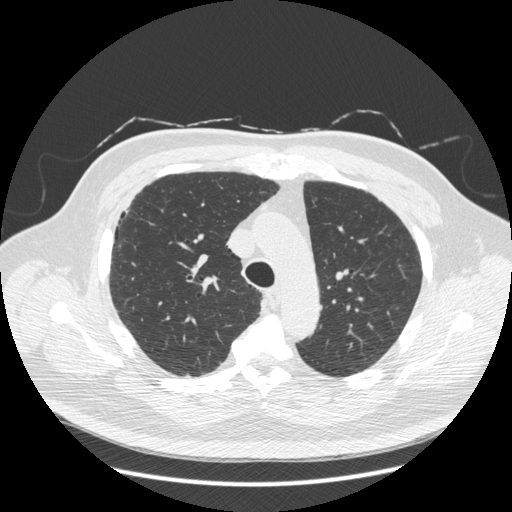
Axial slice from a low-dose chest CT screening exam; second annual screen; lung window (W 1500 / L -600 HU); 1.25 mm slice thickness; standard (soft-tissue) reconstruction kernel (STANDARD); 120 kVp; slice 74 of 281 in the series; 512 × 512 image matrix. Male participant, aged 66 years at enrolment. Current smoker at enrolment.
• Lesion marked by an expert reader, bounding box <99,211,144,259> (left, top, right, bottom; pixels).
• The screening reader recorded 2 non-calcified nodules or masses ≥4 mm on this exam (right lower lobe, right lower lobe); which of them this box marks is not recorded.
• Participant outcome: lung cancer diagnosed 403 days after this screen — non-small cell carcinoma, right upper lobe, stage IV (AJCC 6th edition), 50 mm at pathology.